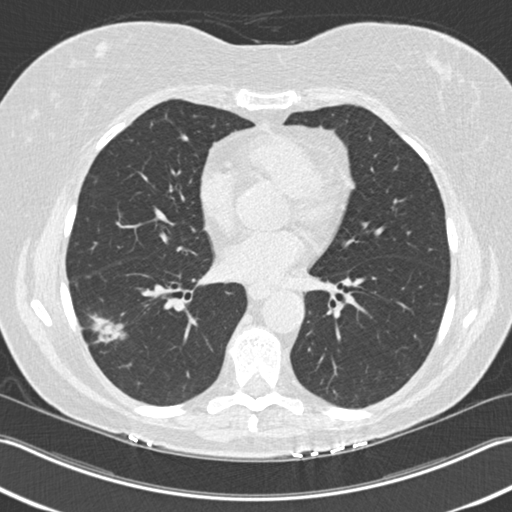
Low-dose screening chest CT, axial slice. Baseline annual screen. Lung window (W 1500 / L -600 HU). 2 mm slice thickness. Standard (soft-tissue) reconstruction kernel (B30f). Female, age 63 years at enrolment. Current smoker at enrolment.
• Expert reader's lesion annotation, bounding box <67,308,133,370> (left, top, right, bottom; pixels).
• The screening reader recorded 3 non-calcified nodules or masses ≥4 mm on this exam (right upper lobe, right lower lobe, right lower lobe); which of them this box marks is not recorded.
• Official screen result: positive, change unspecified: nodule(s) >= 4 mm or enlarging nodule(s), mass(es), or other non-specific abnormalities suspicious for lung cancer.
• Participant outcome: lung cancer diagnosed 57 days after this screen — bronchiolo-alveolar adenocarcinoma, NOS, right lower lobe, well differentiated (G1), stage IA (AJCC 6th edition), 25 mm at pathology.